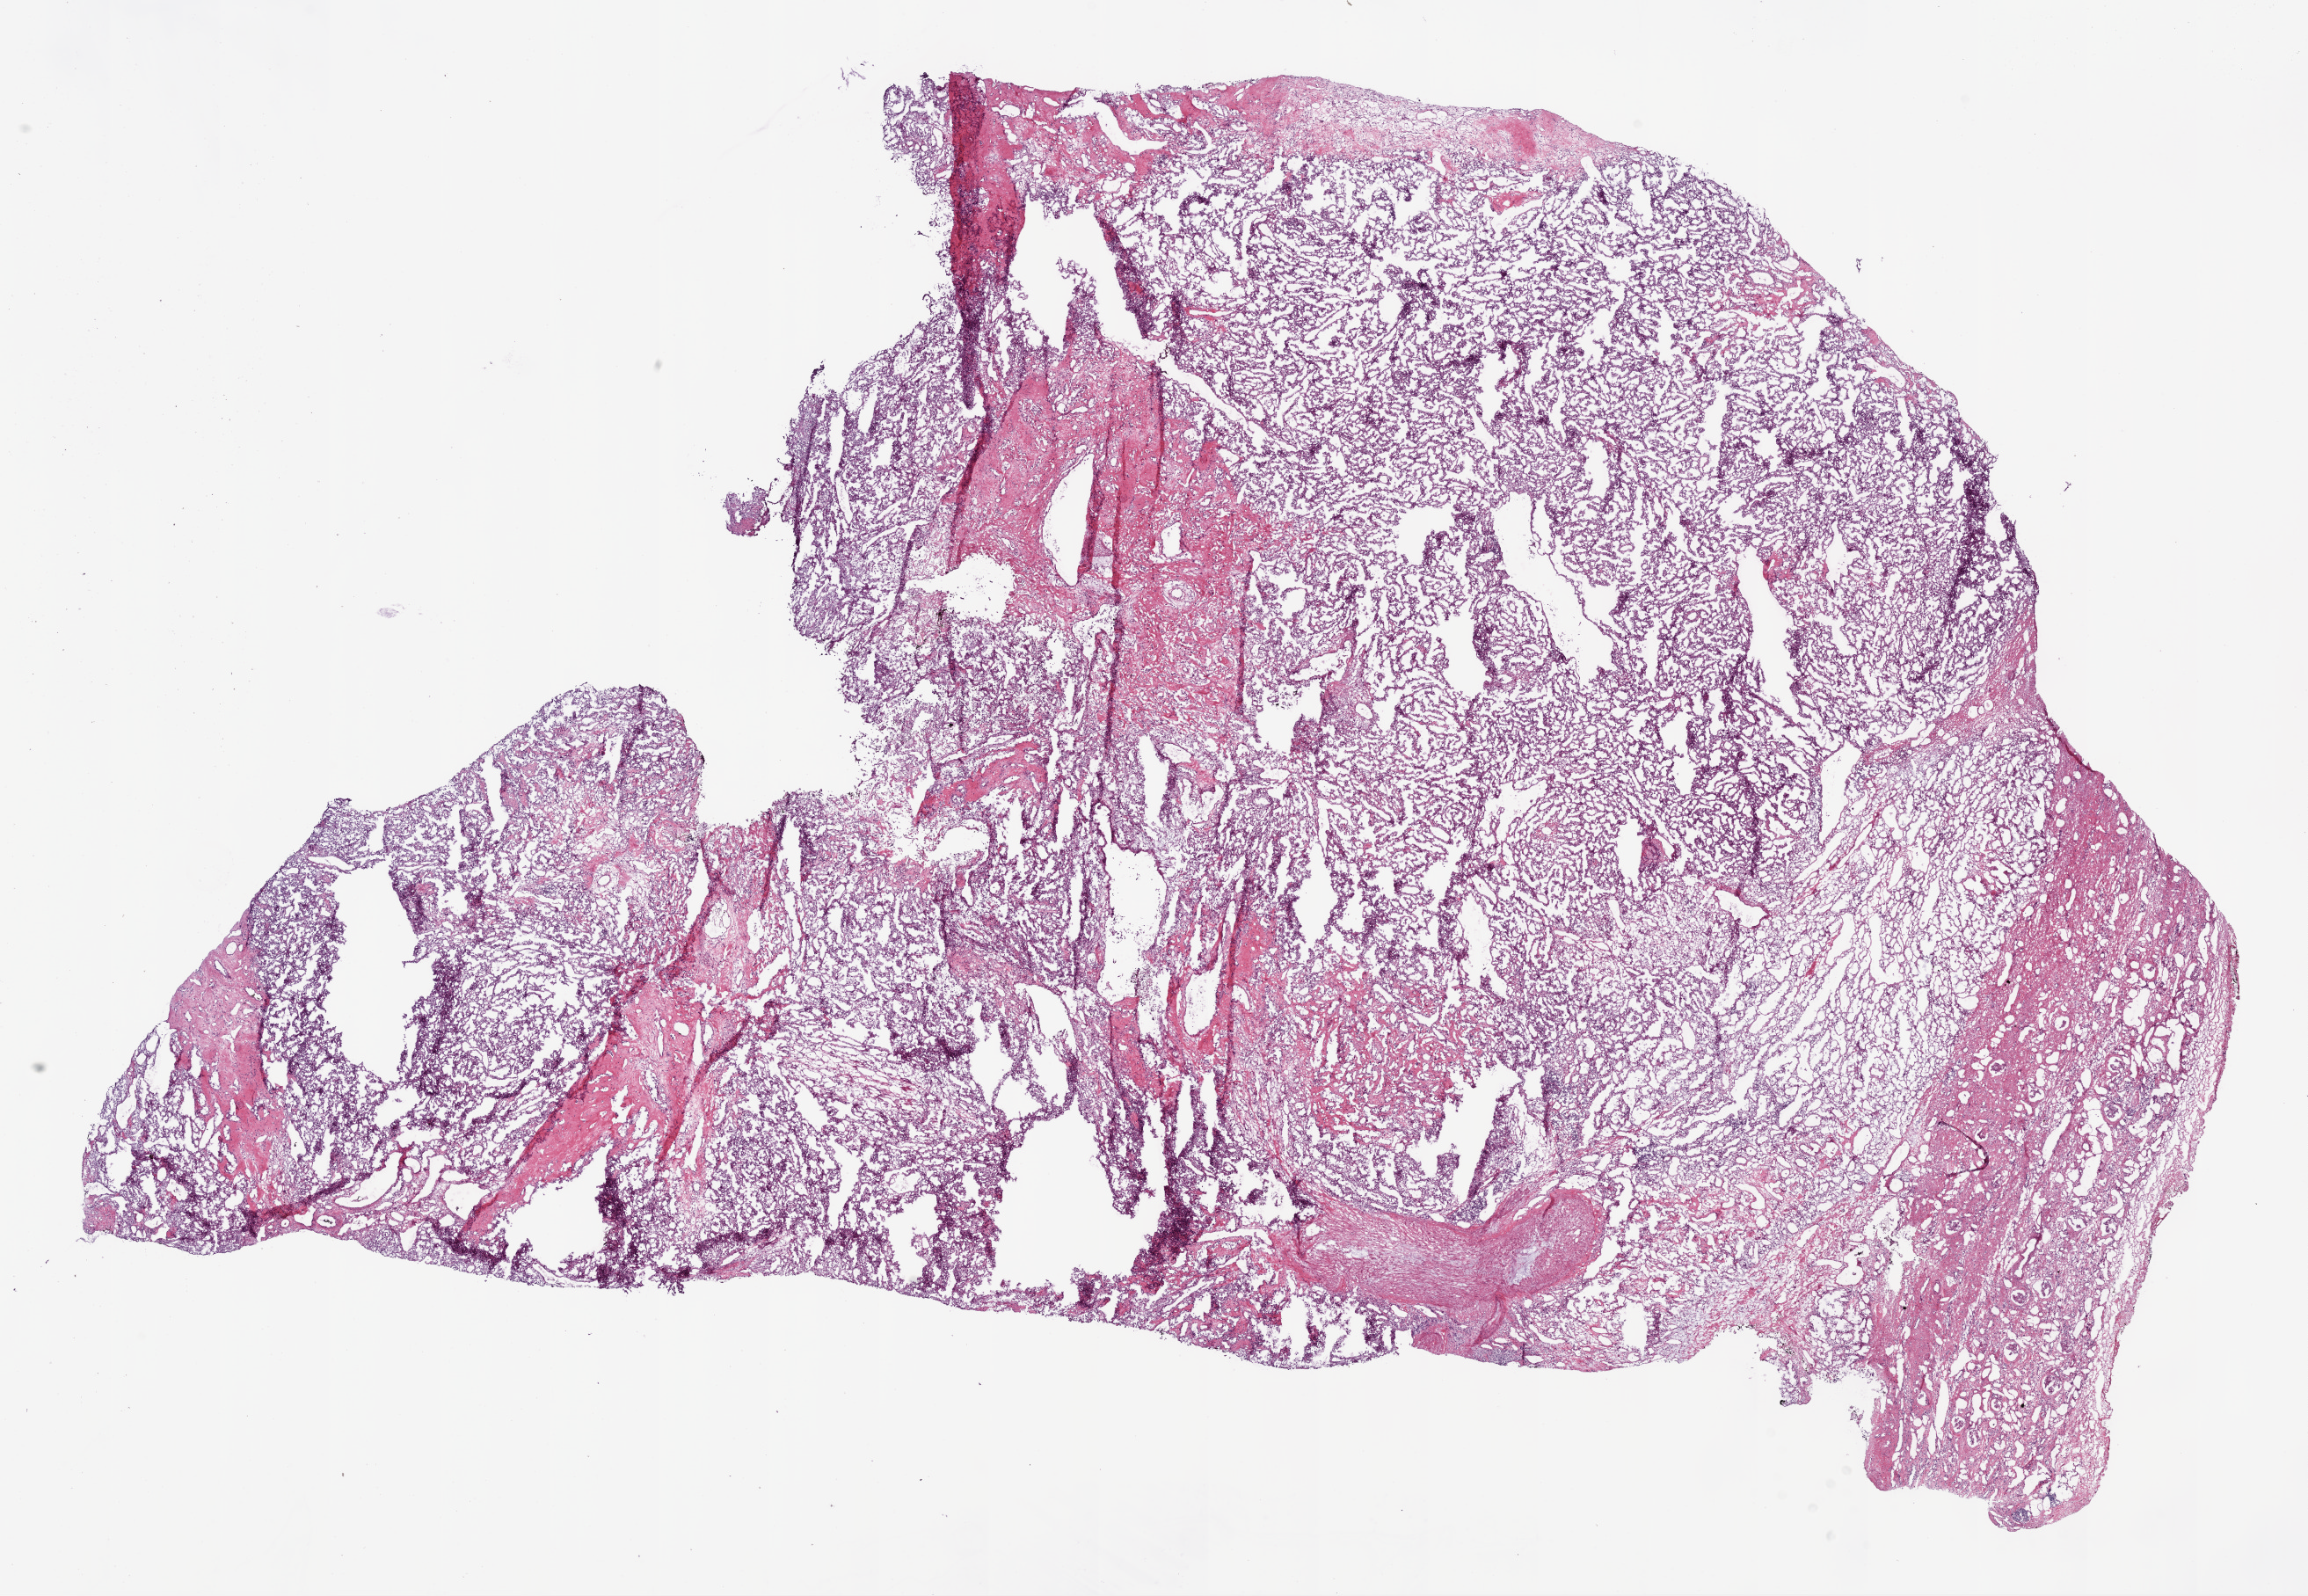
H&E whole-slide image — low-resolution overview of the scanned area, about 21.1 x 14.6 mm (slide scanned at 20x), frozen section, sample: primary tumour, kidney. Male, age 53 years at initial diagnosis. Histologic grade: G2 (moderately differentiated). Composition of this section per pathologist review: tumour cells 75%, tumour nuclei 80%, normal cells 10%, stromal cells 15%, necrosis 0%.
Pathologic diagnosis: Clear cell adenocarcinoma, NOS. AJCC pathologic stage: I.